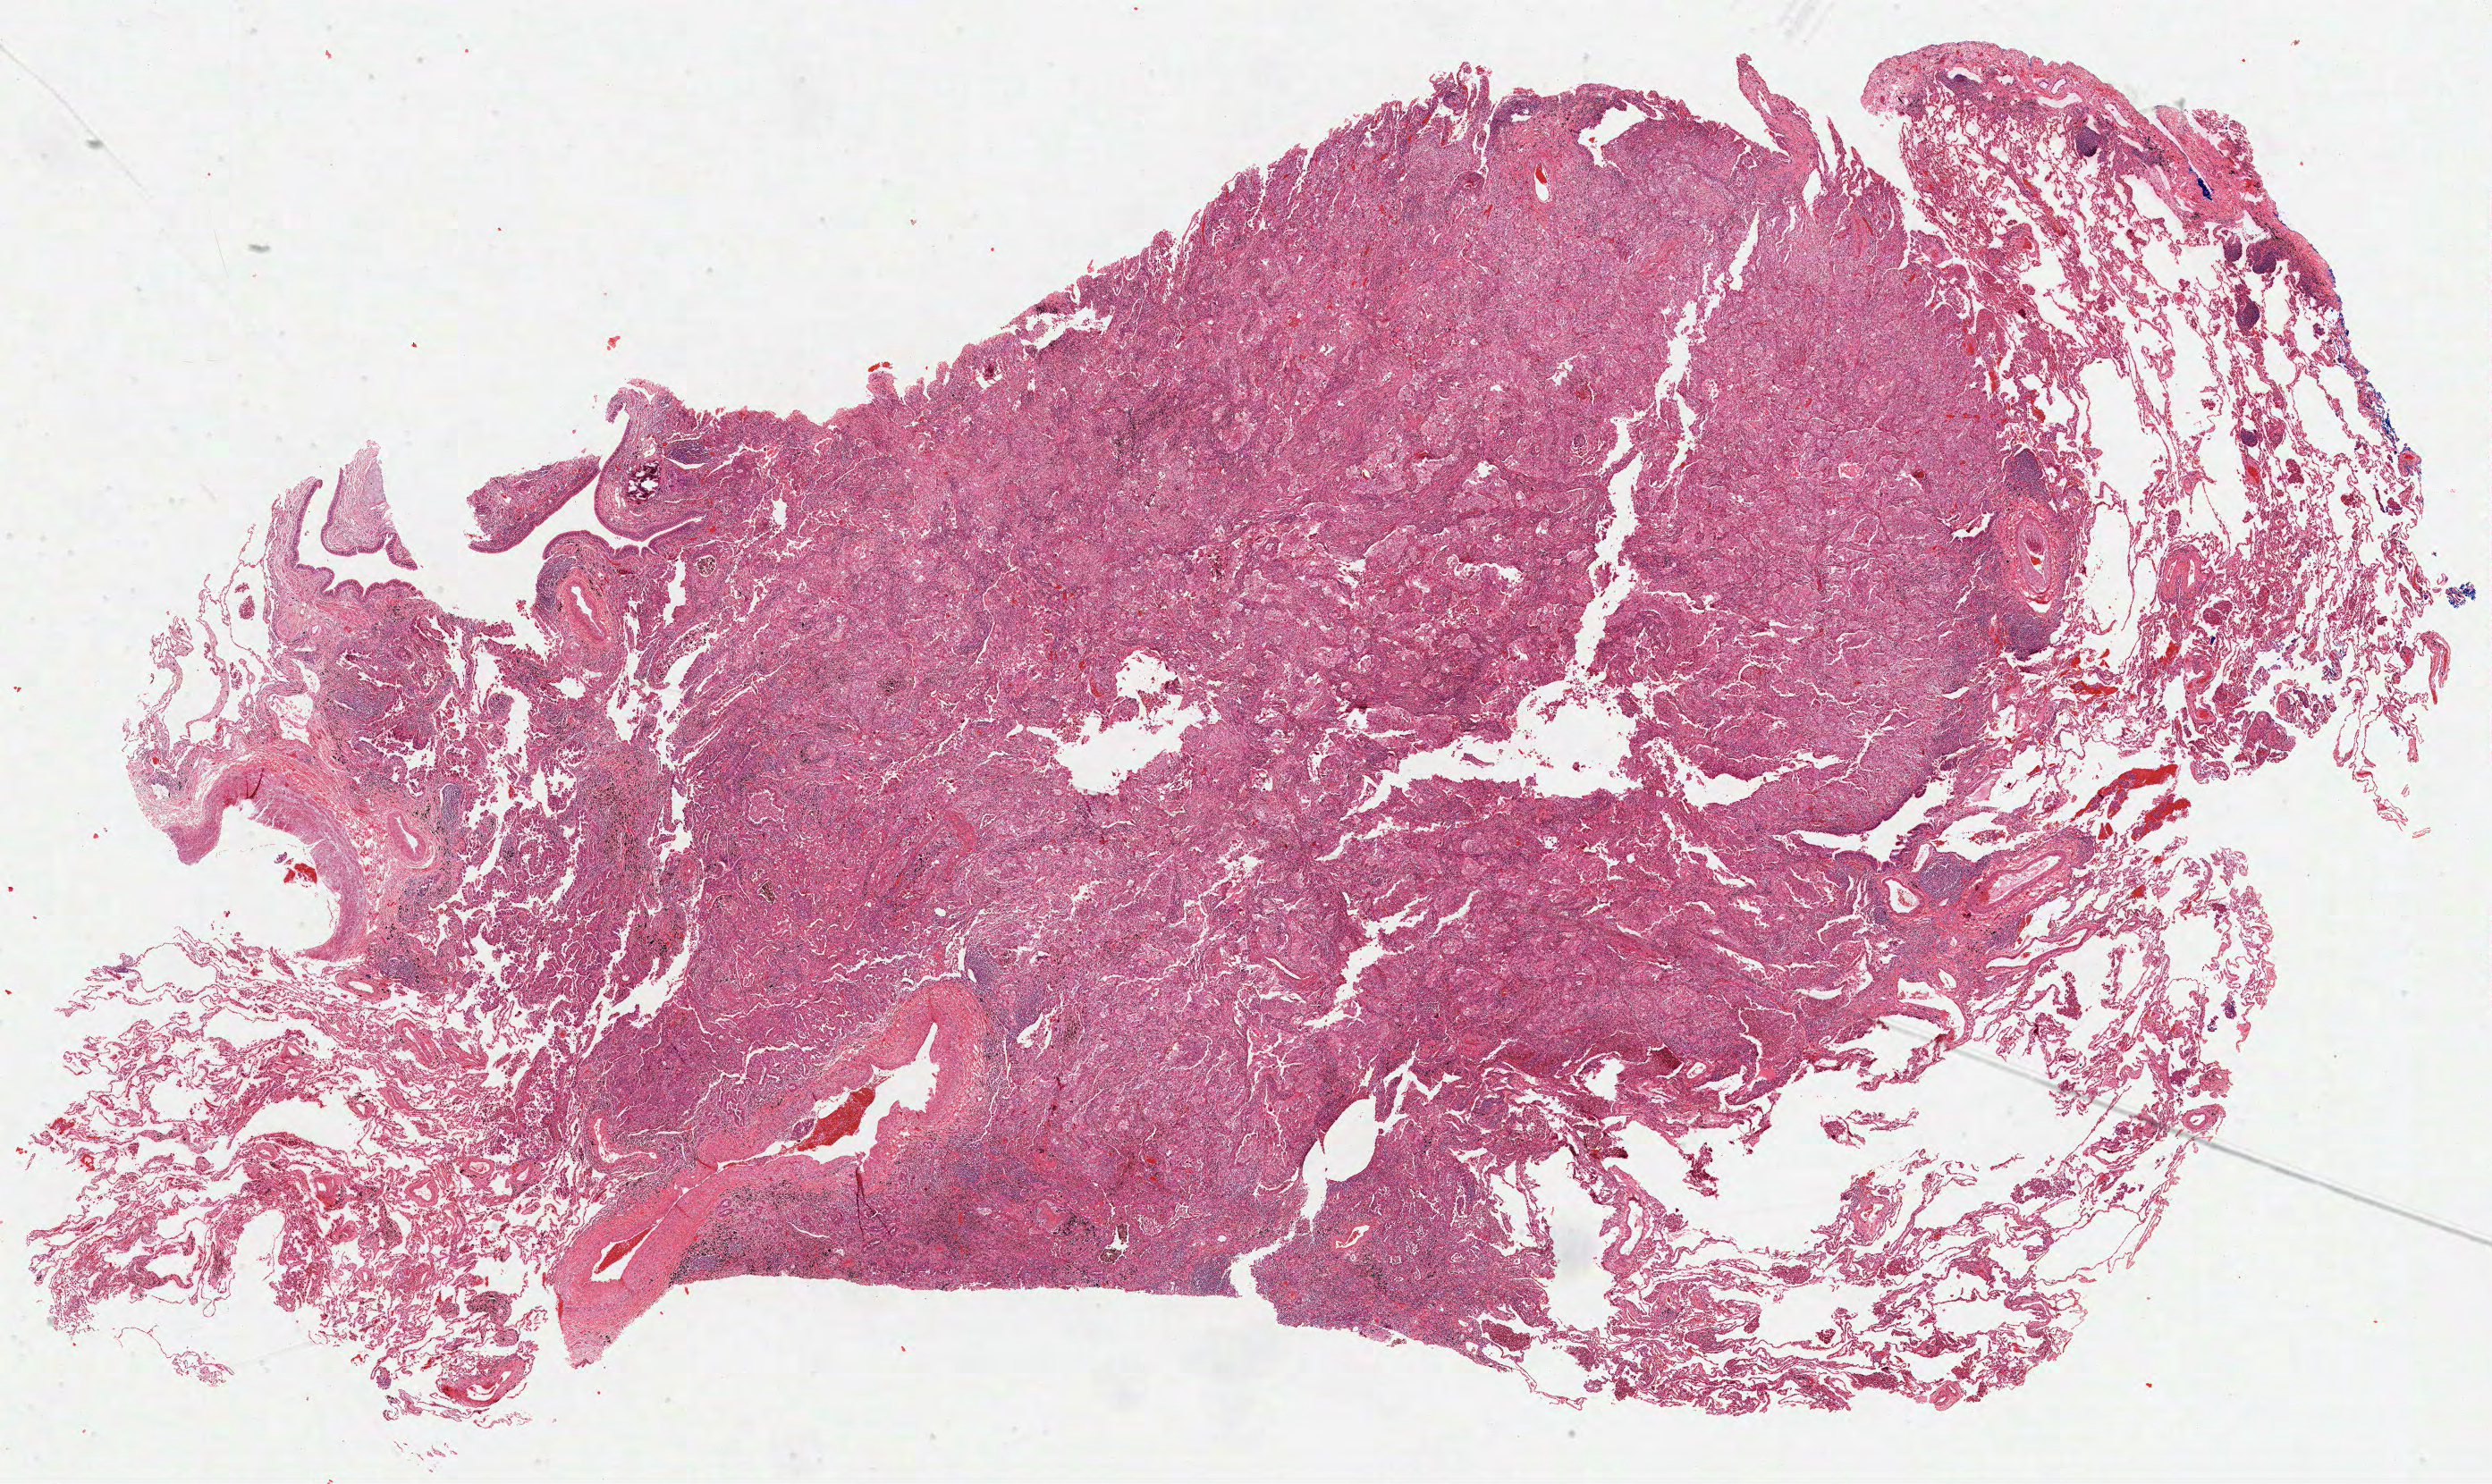
Digitized H&E tissue section (whole slide), whole scanned area (about 22.5 x 13.4 mm, from a 40x scan) shown as a low-resolution overview; formalin-fixed paraffin-embedded (FFPE) diagnostic section; lung, primary tumour sample. Female patient; age at initial diagnosis 57 years.
Diagnosis: Adenocarcinoma, NOS (lower lobe, lung).